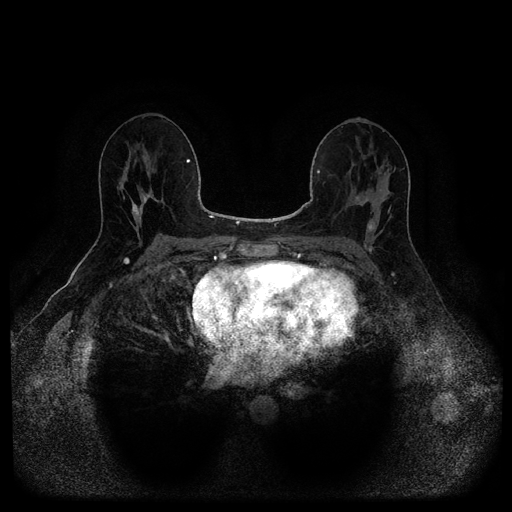
Breast MRI (dynamic contrast-enhanced, multi-phase), one axial slice. Slice 59 of 116 in the series (ordered by position). Dynamic contrast-enhanced series, time point 2 of 5 at this slice position (early post-contrast). 1.5 T. TE 2.6 ms, TR 5.3 ms. 2.2 mm slice thickness. 512 × 512 image matrix. Patient: female, 49 years.
Outlined on this slice (semi-automatically segmented with operator editing):
- breast lesion (labelled benign in the annotation): bounding box <366,217,378,234> (left, top, right, bottom; pixels)